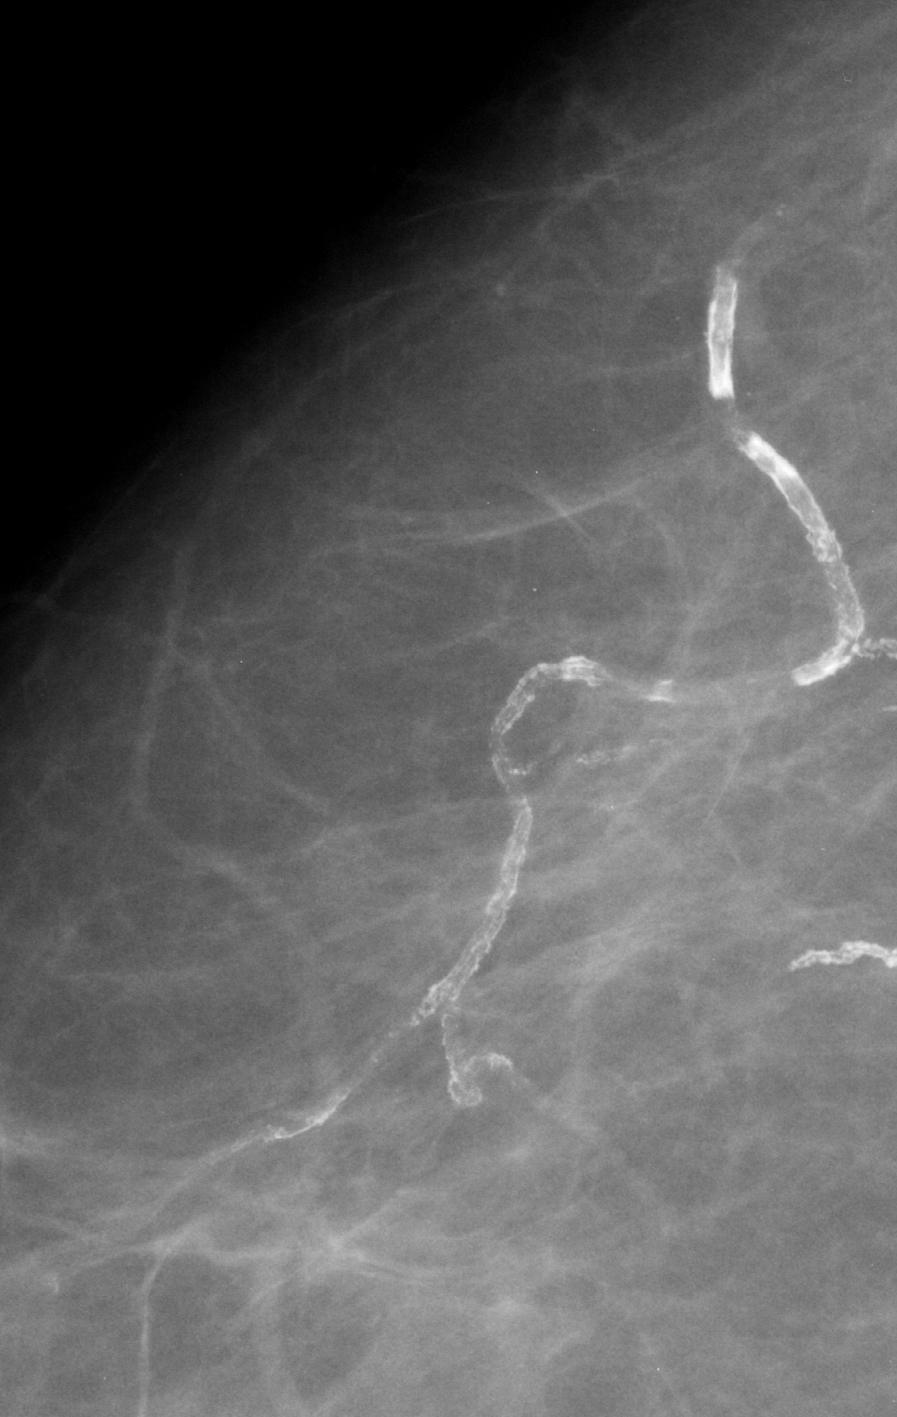
Cropped region of a digitized screen-film mammogram centred on a radiologist-marked abnormality; right breast; CC view; BI-RADS breast density category 1 (scale 1–4).
Marked abnormality: calcifications, morphology vascular; BI-RADS assessment category 2; subtlety rating 4 on a 1 (subtle) to 5 (obvious) scale; benign; no additional work-up was recommended (benign without callback).